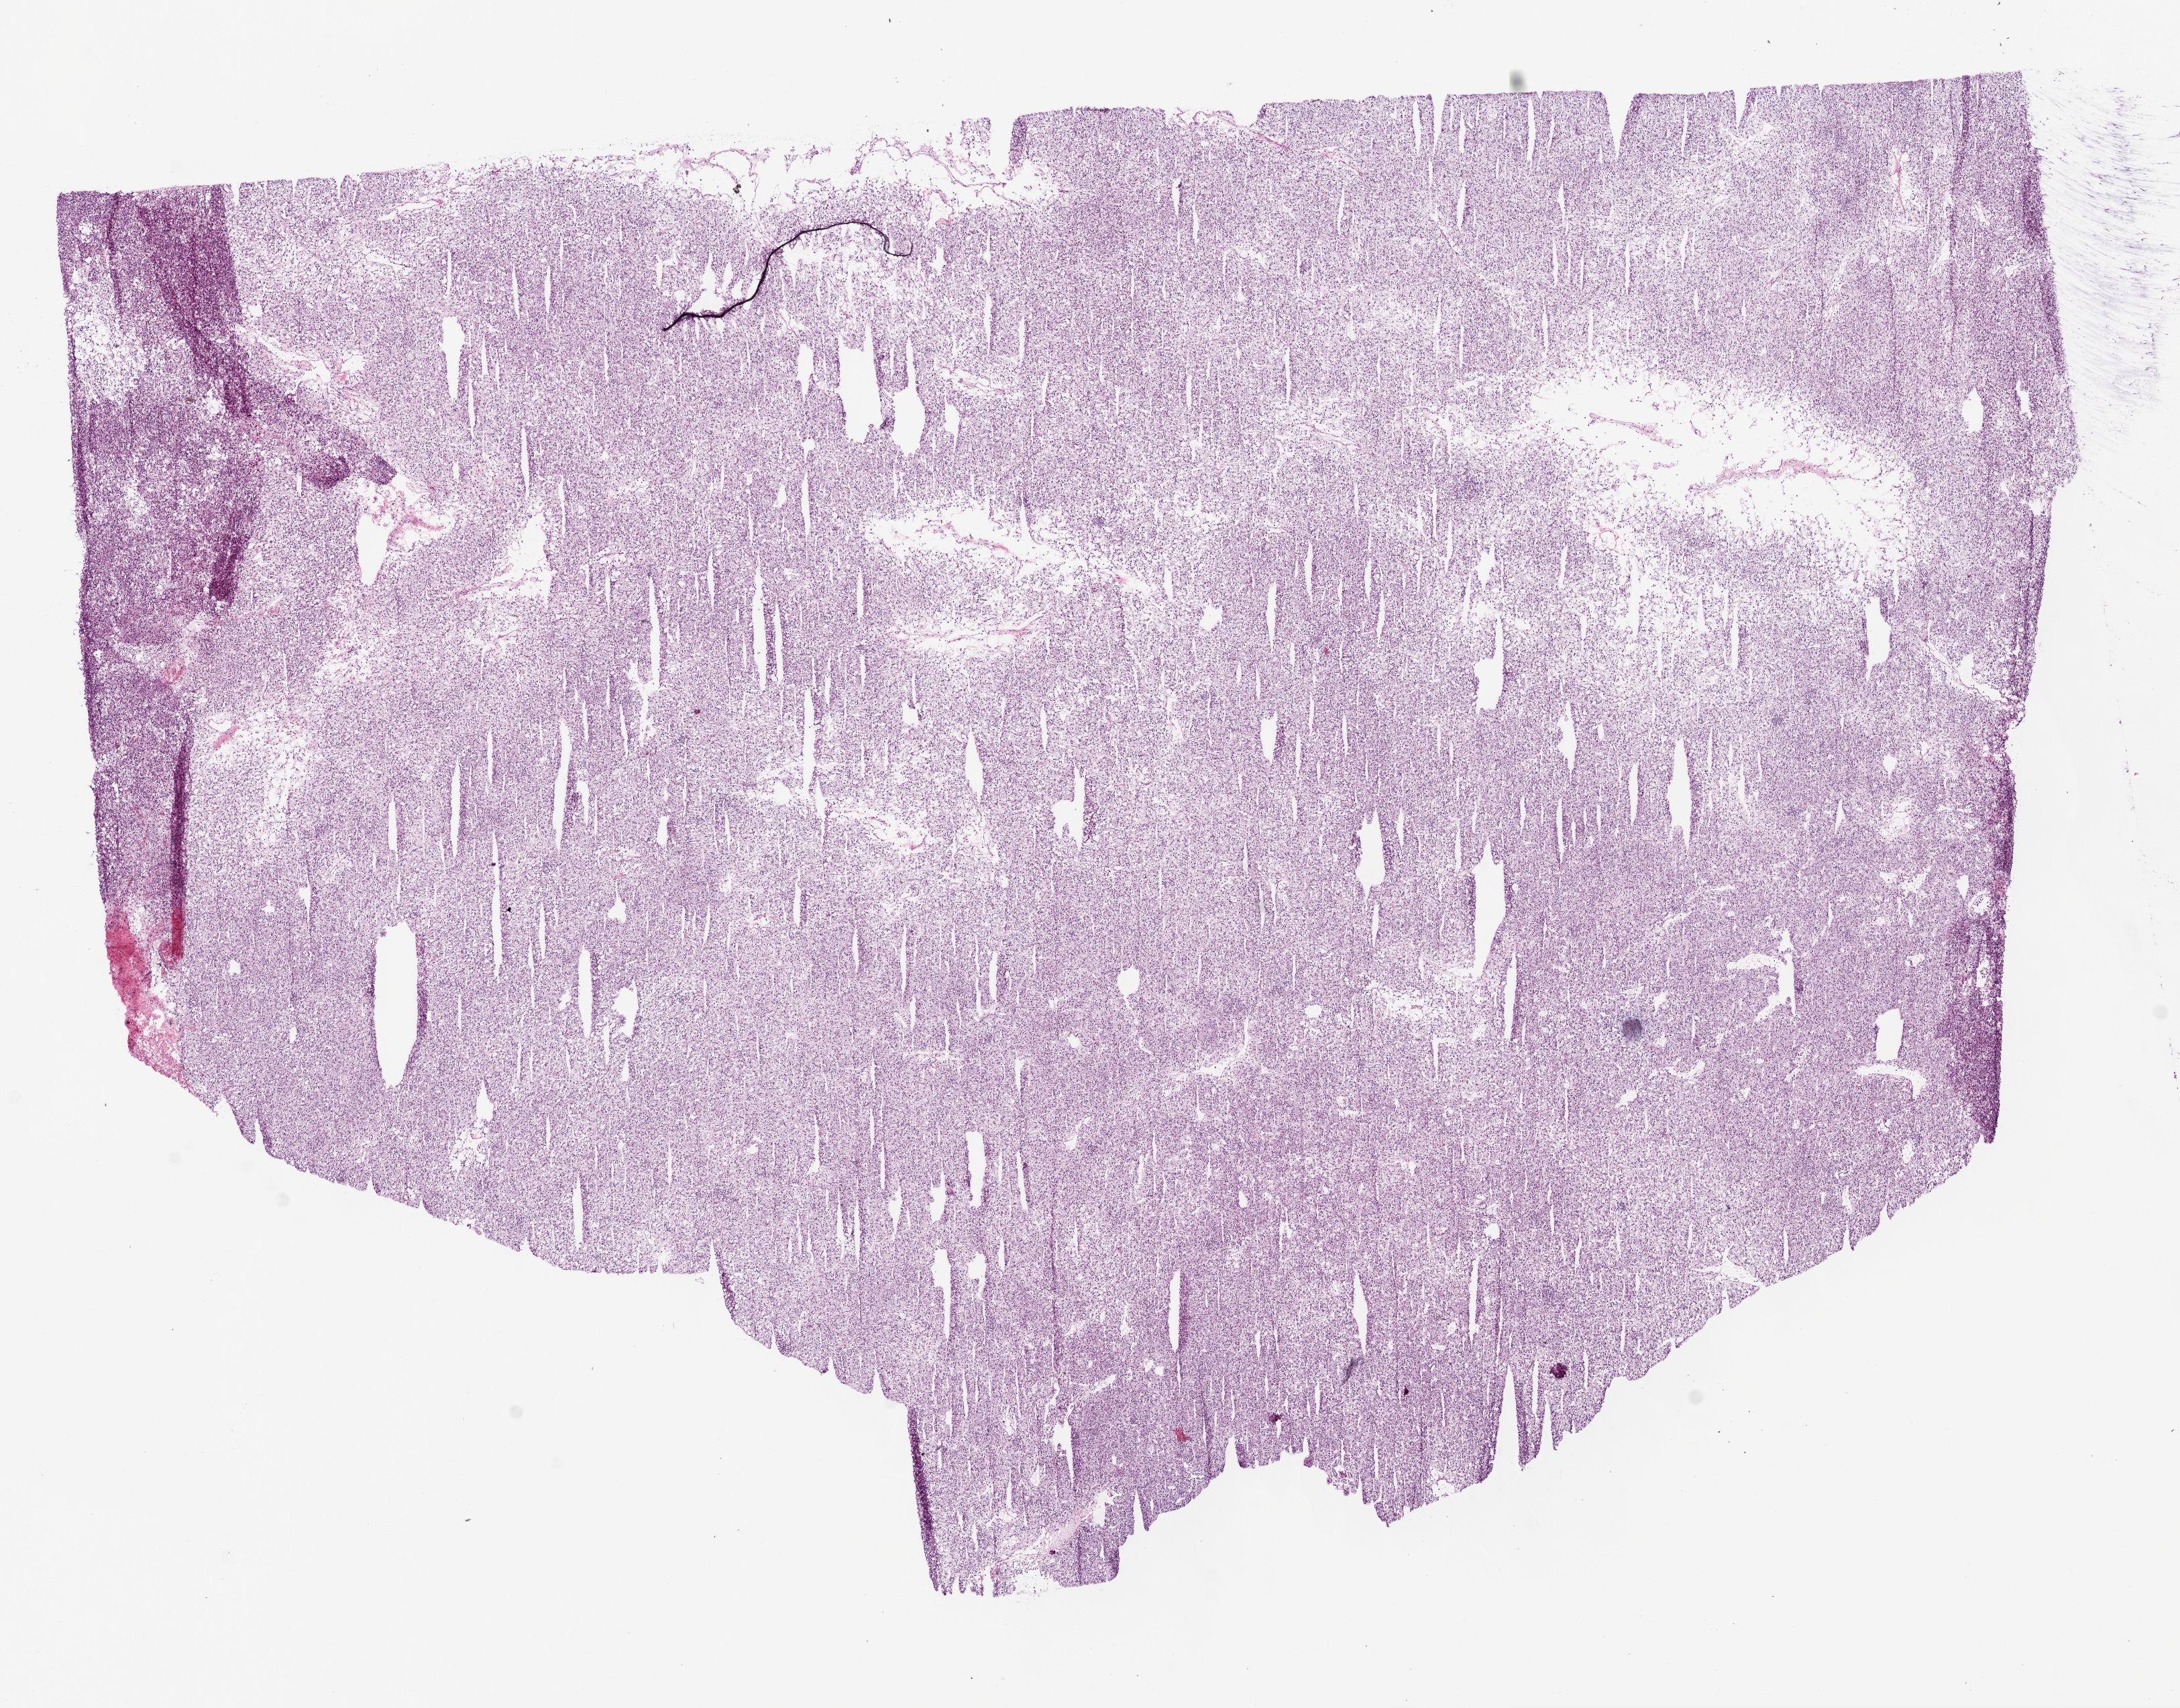
Hematoxylin and eosin (H&E) stained whole-slide image — whole scanned area (about 13.0 x 10.2 mm, from a 20x scan) shown as a low-resolution overview, frozen section, kidney, primary tumour sample. Male patient; age at initial diagnosis 61 years. Histologic grade: G2 (moderately differentiated). Slide review estimates, as recorded: tumour cells 100%, tumour nuclei 99%, normal cells 0%, stromal cells 0%, necrosis 0%. Infiltration values recorded for this section: lymphocyte infiltration 1%.
AJCC pathologic stage: I. Histologic diagnosis: Clear cell adenocarcinoma, NOS.